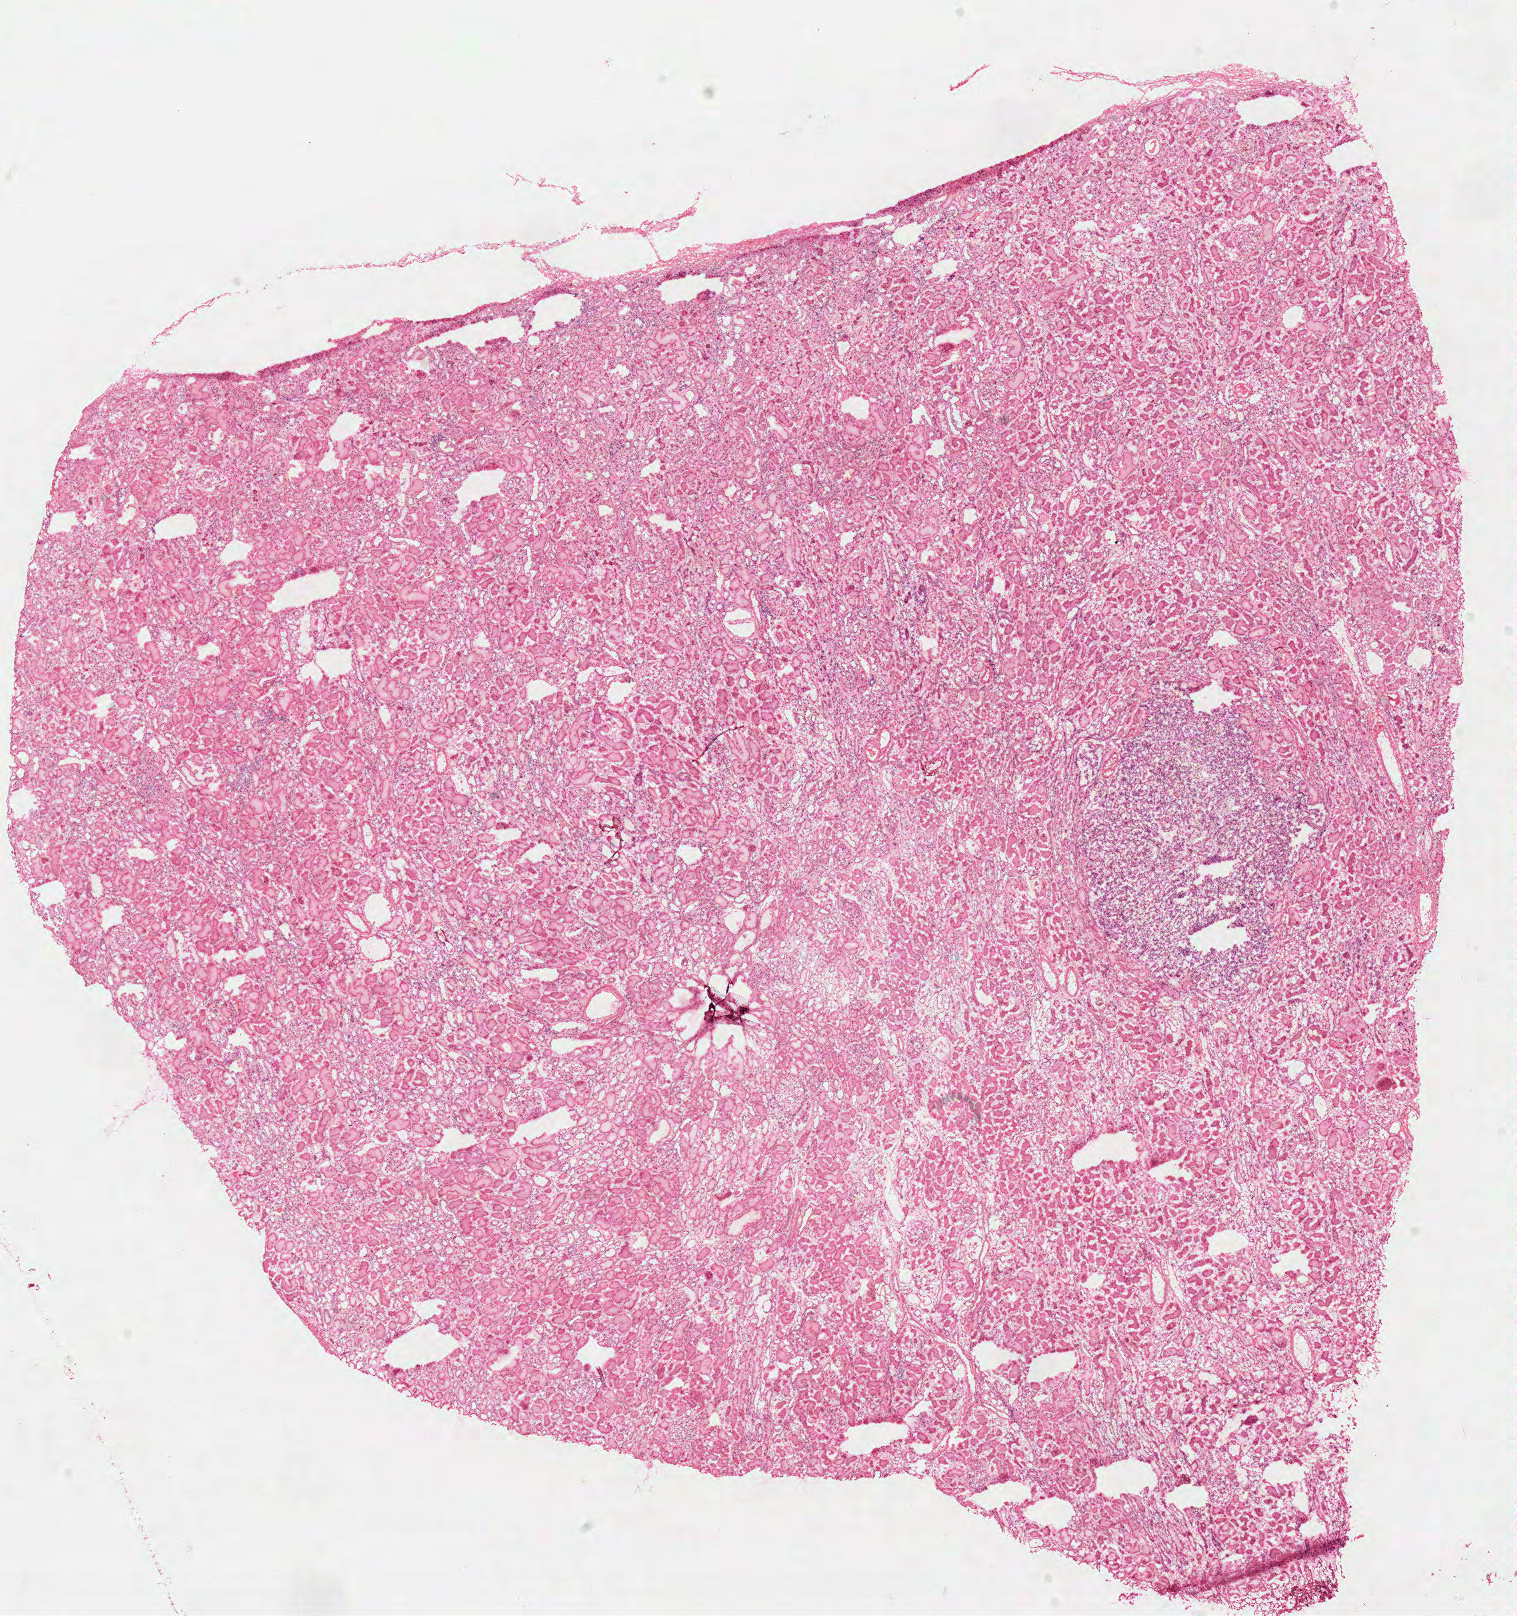
Hematoxylin and eosin (H&E) stained whole-slide image — low-resolution overview of the scanned area, about 12.0 x 12.7 mm; frozen section from the top of the tissue portion; solid tissue normal (non-tumour tissue) sample from the kidney. Male, age 63 years at initial diagnosis.
This section: solid tissue normal (non-tumour) sample from the same patient. Patient diagnosis: Papillary adenocarcinoma, NOS.